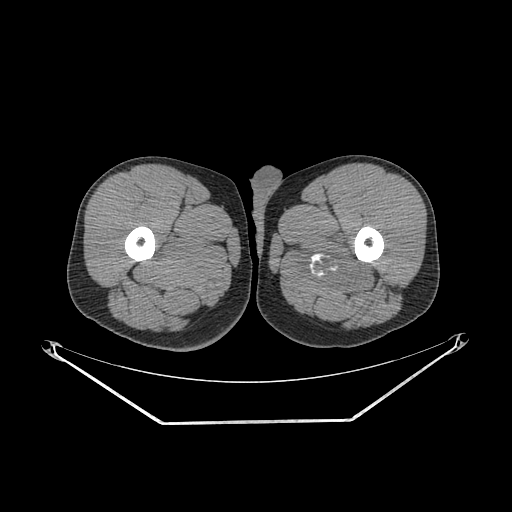
CT of an extremity soft-tissue mass (from a PET/CT study), one axial slice. Position 251 of 267 along the scan axis. 140 kVp. Soft-tissue window (W 400 / L 40 HU). 3.75 mm slice thickness. 512 × 512 image matrix, field of view 500 × 500 mm. Male patient. From the clinical record (not read from this slice): histological type: extraskeletal osteosarcoma; grade: high; site of the primary tumour: left adductur.
Outlined on this slice (expert contour drawn on MRI and transferred to this co-registered scan by the dataset authors):
- gross tumour volume (mass): bounding box <290,226,378,296> (left, top, right, bottom; pixels)